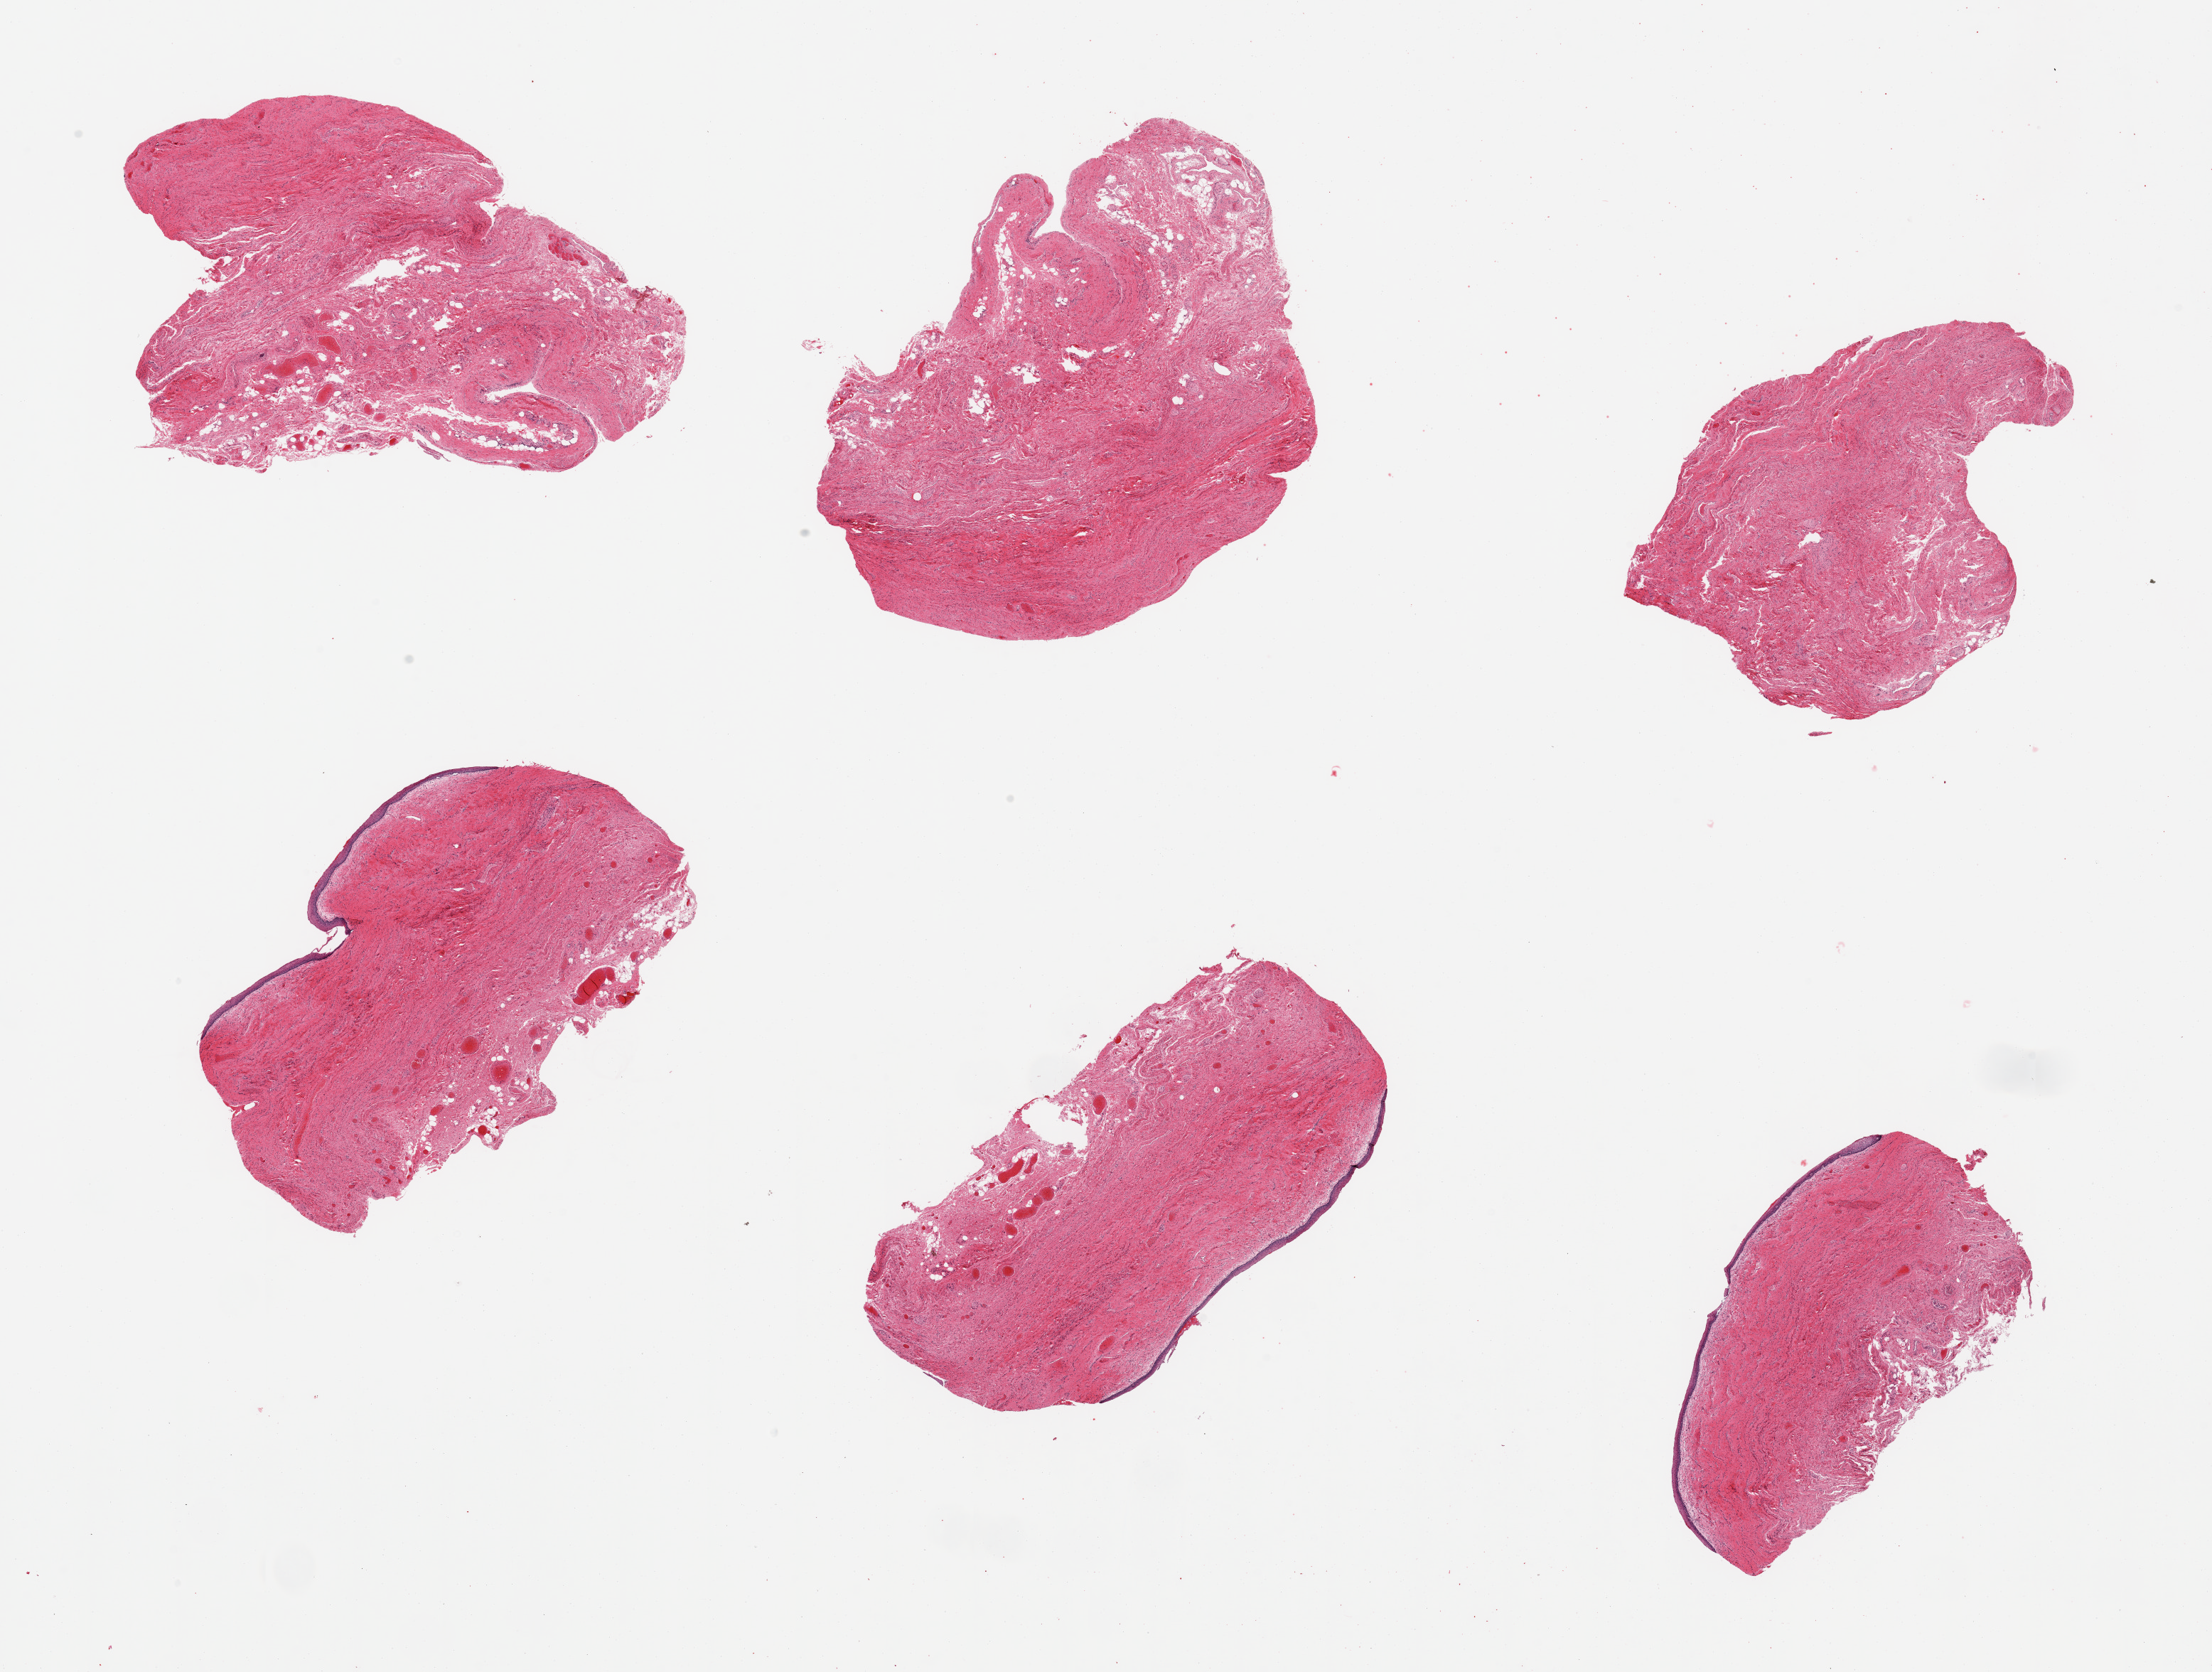
Haematoxylin and eosin whole-slide image, brightfield, shown as a low-resolution overview of the whole scanned area (about 24.6 x 18.6 mm). PAXgene-fixed paraffin-embedded (PFPE) section. Target tissue: vagina. Donor tissue sample. Female donor.
Review note (as recorded): 6 pieces: 3 have sloughed epithelium.